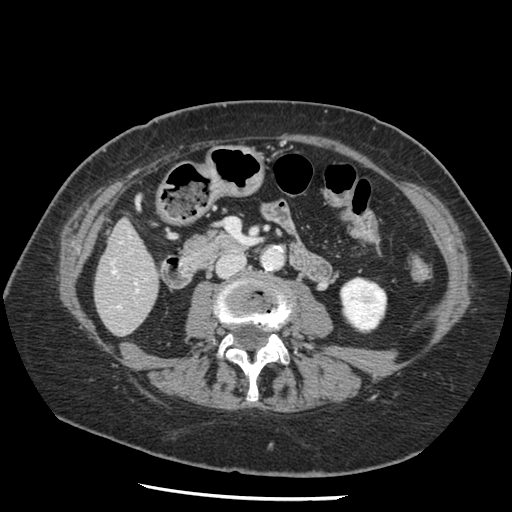
Contrast-enhanced abdominal CT, one axial slice. 120 kVp. Soft-tissue window (W 400 / L 40 HU). 2.5 mm slice thickness. 512 × 512 image matrix. Female patient, age 85 years. From the clinical record (not read from this slice): diagnosis: colorectal cancer liver metastases, imaged before liver resection; multiple liver metastases: no; largest metastasis: 0.9 cm.
Annotated regions visible in this slice (outlined manually by an expert reader):
- hepatic veins: bounding box (x1, y1, x2, y2) in pixels: (112, 271, 120, 308)
- liver: (96, 222, 159, 335)
- planned liver remnant (the part of the liver to remain after resection): (96, 222, 159, 332)